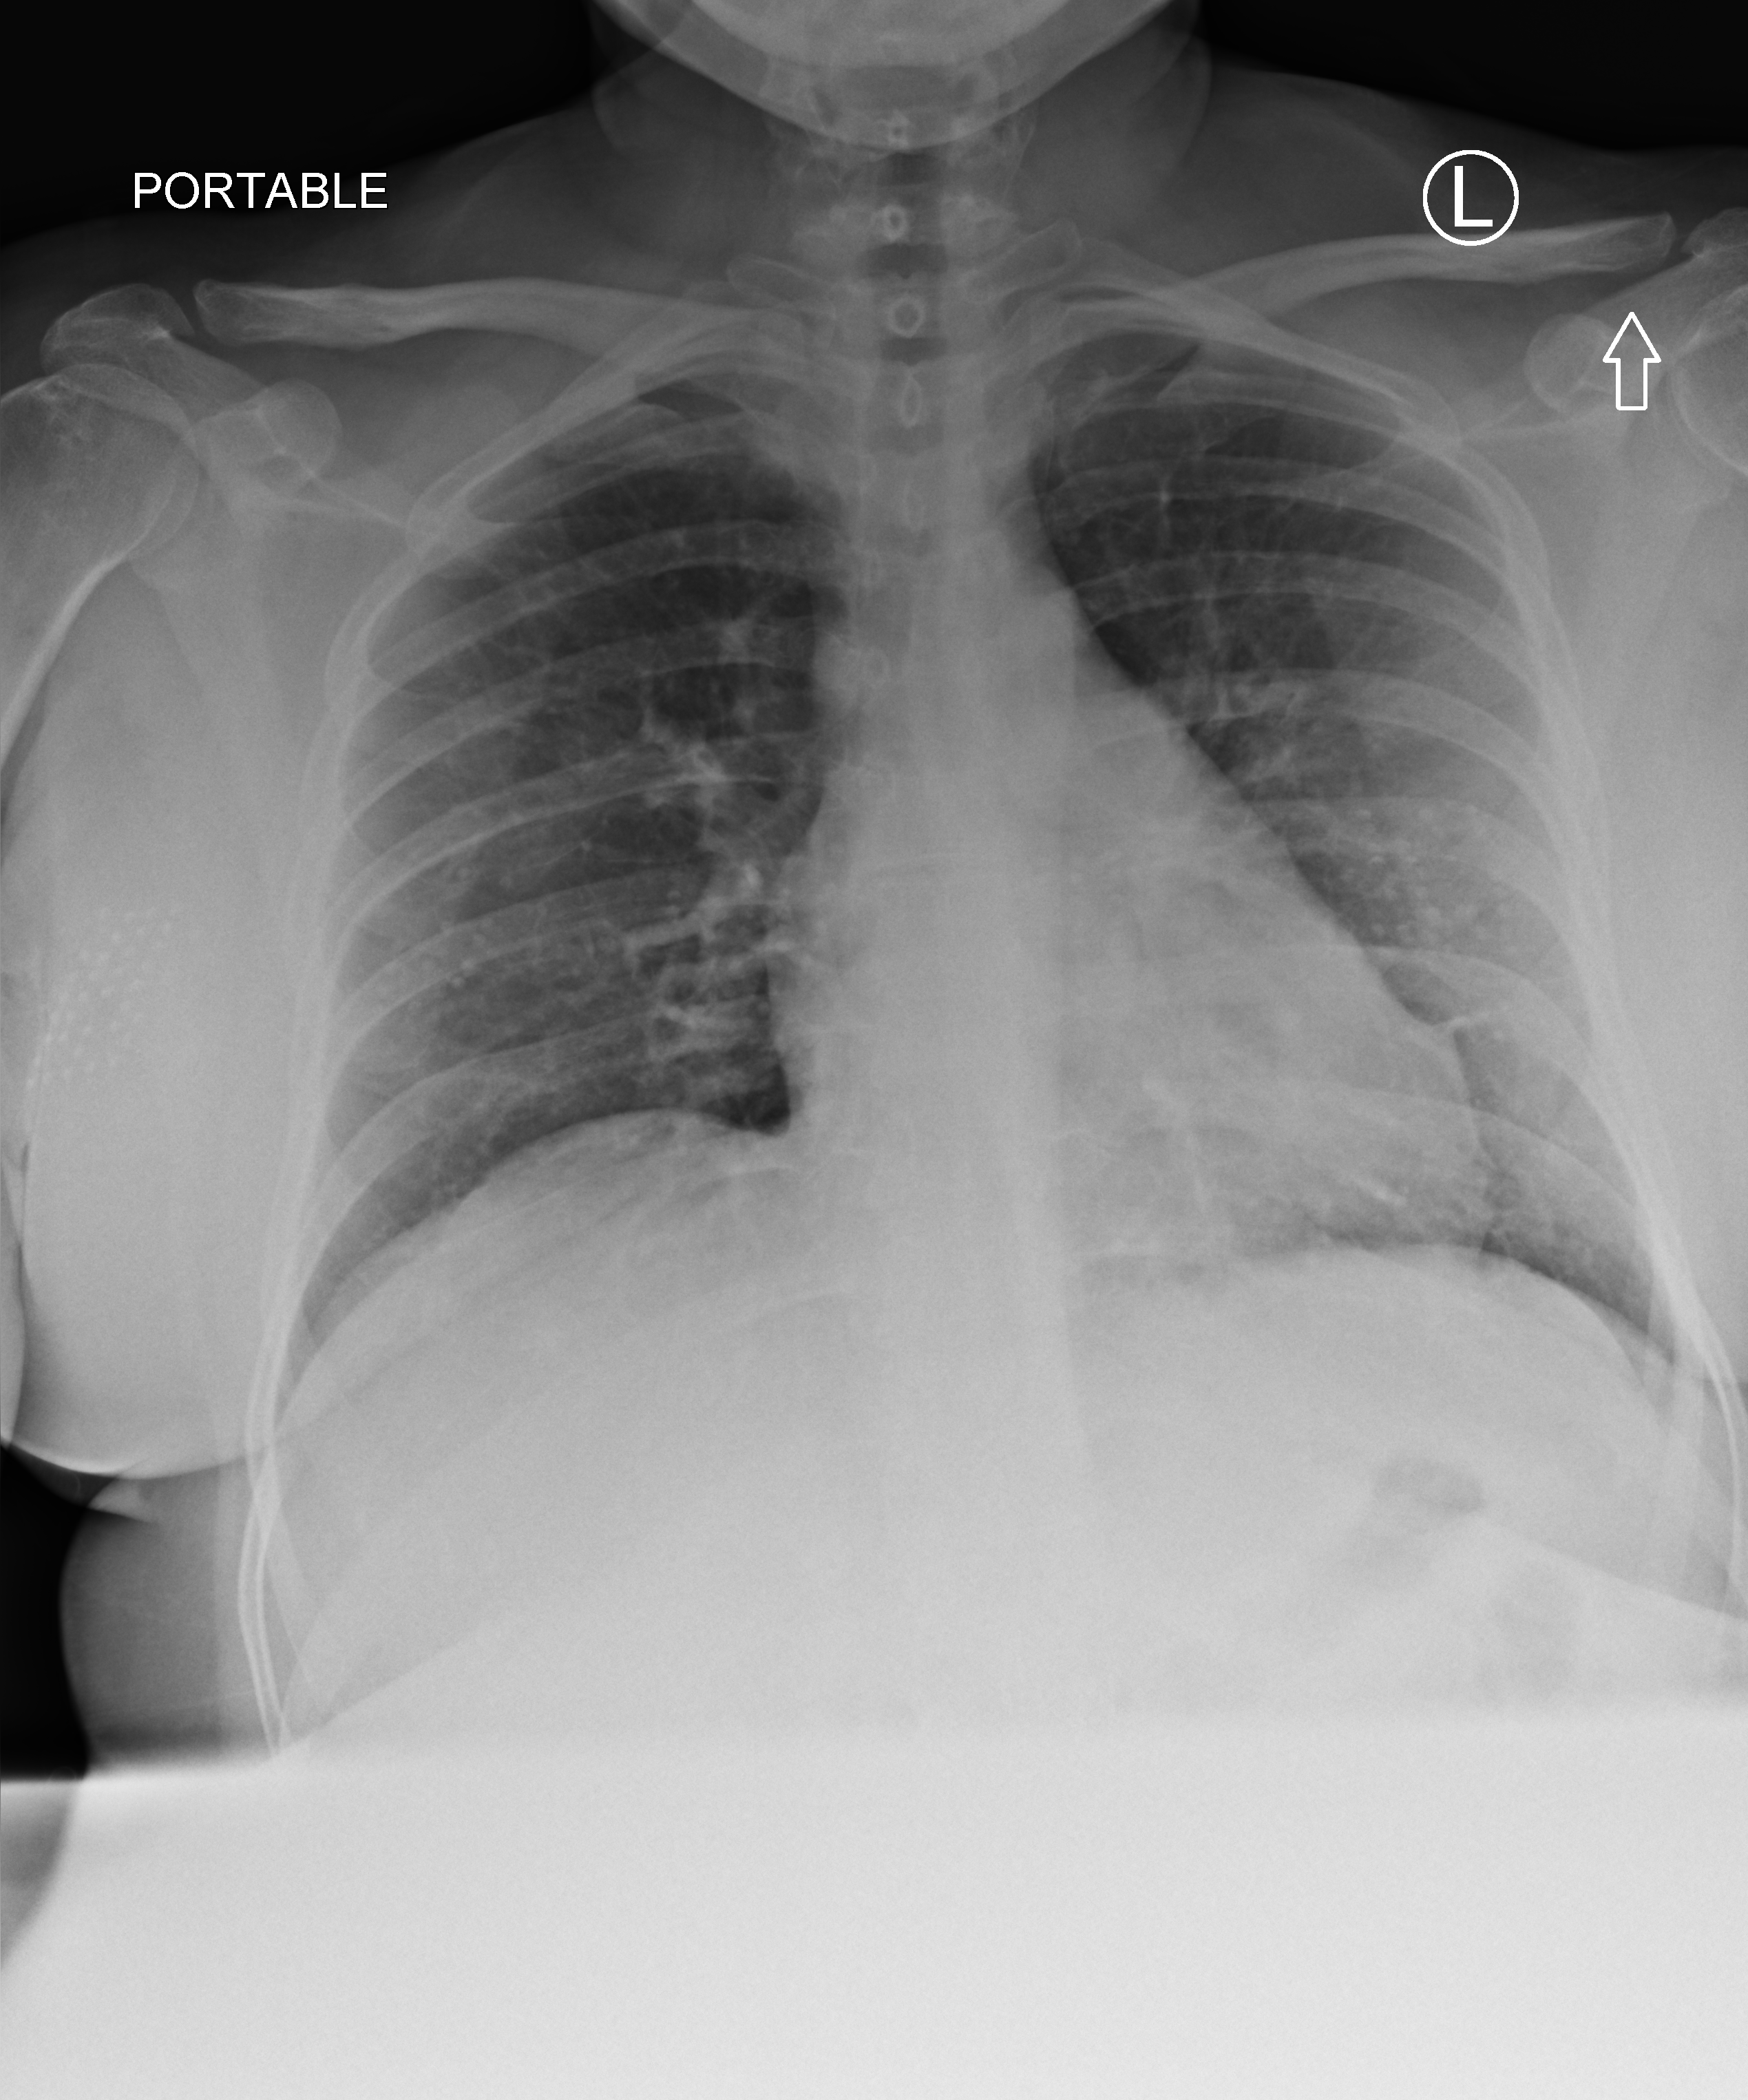
Portable chest radiograph, anteroposterior (AP) projection. Patient hospitalised with COVID-19; female, aged 18–59 years.
Hospital-stay facts (about this admission, not read from this image; timing relative to this image not recorded): COPD (admission record): no; other chronic lung disease (admission record): no; admitted to intensive care during this hospital stay: no.